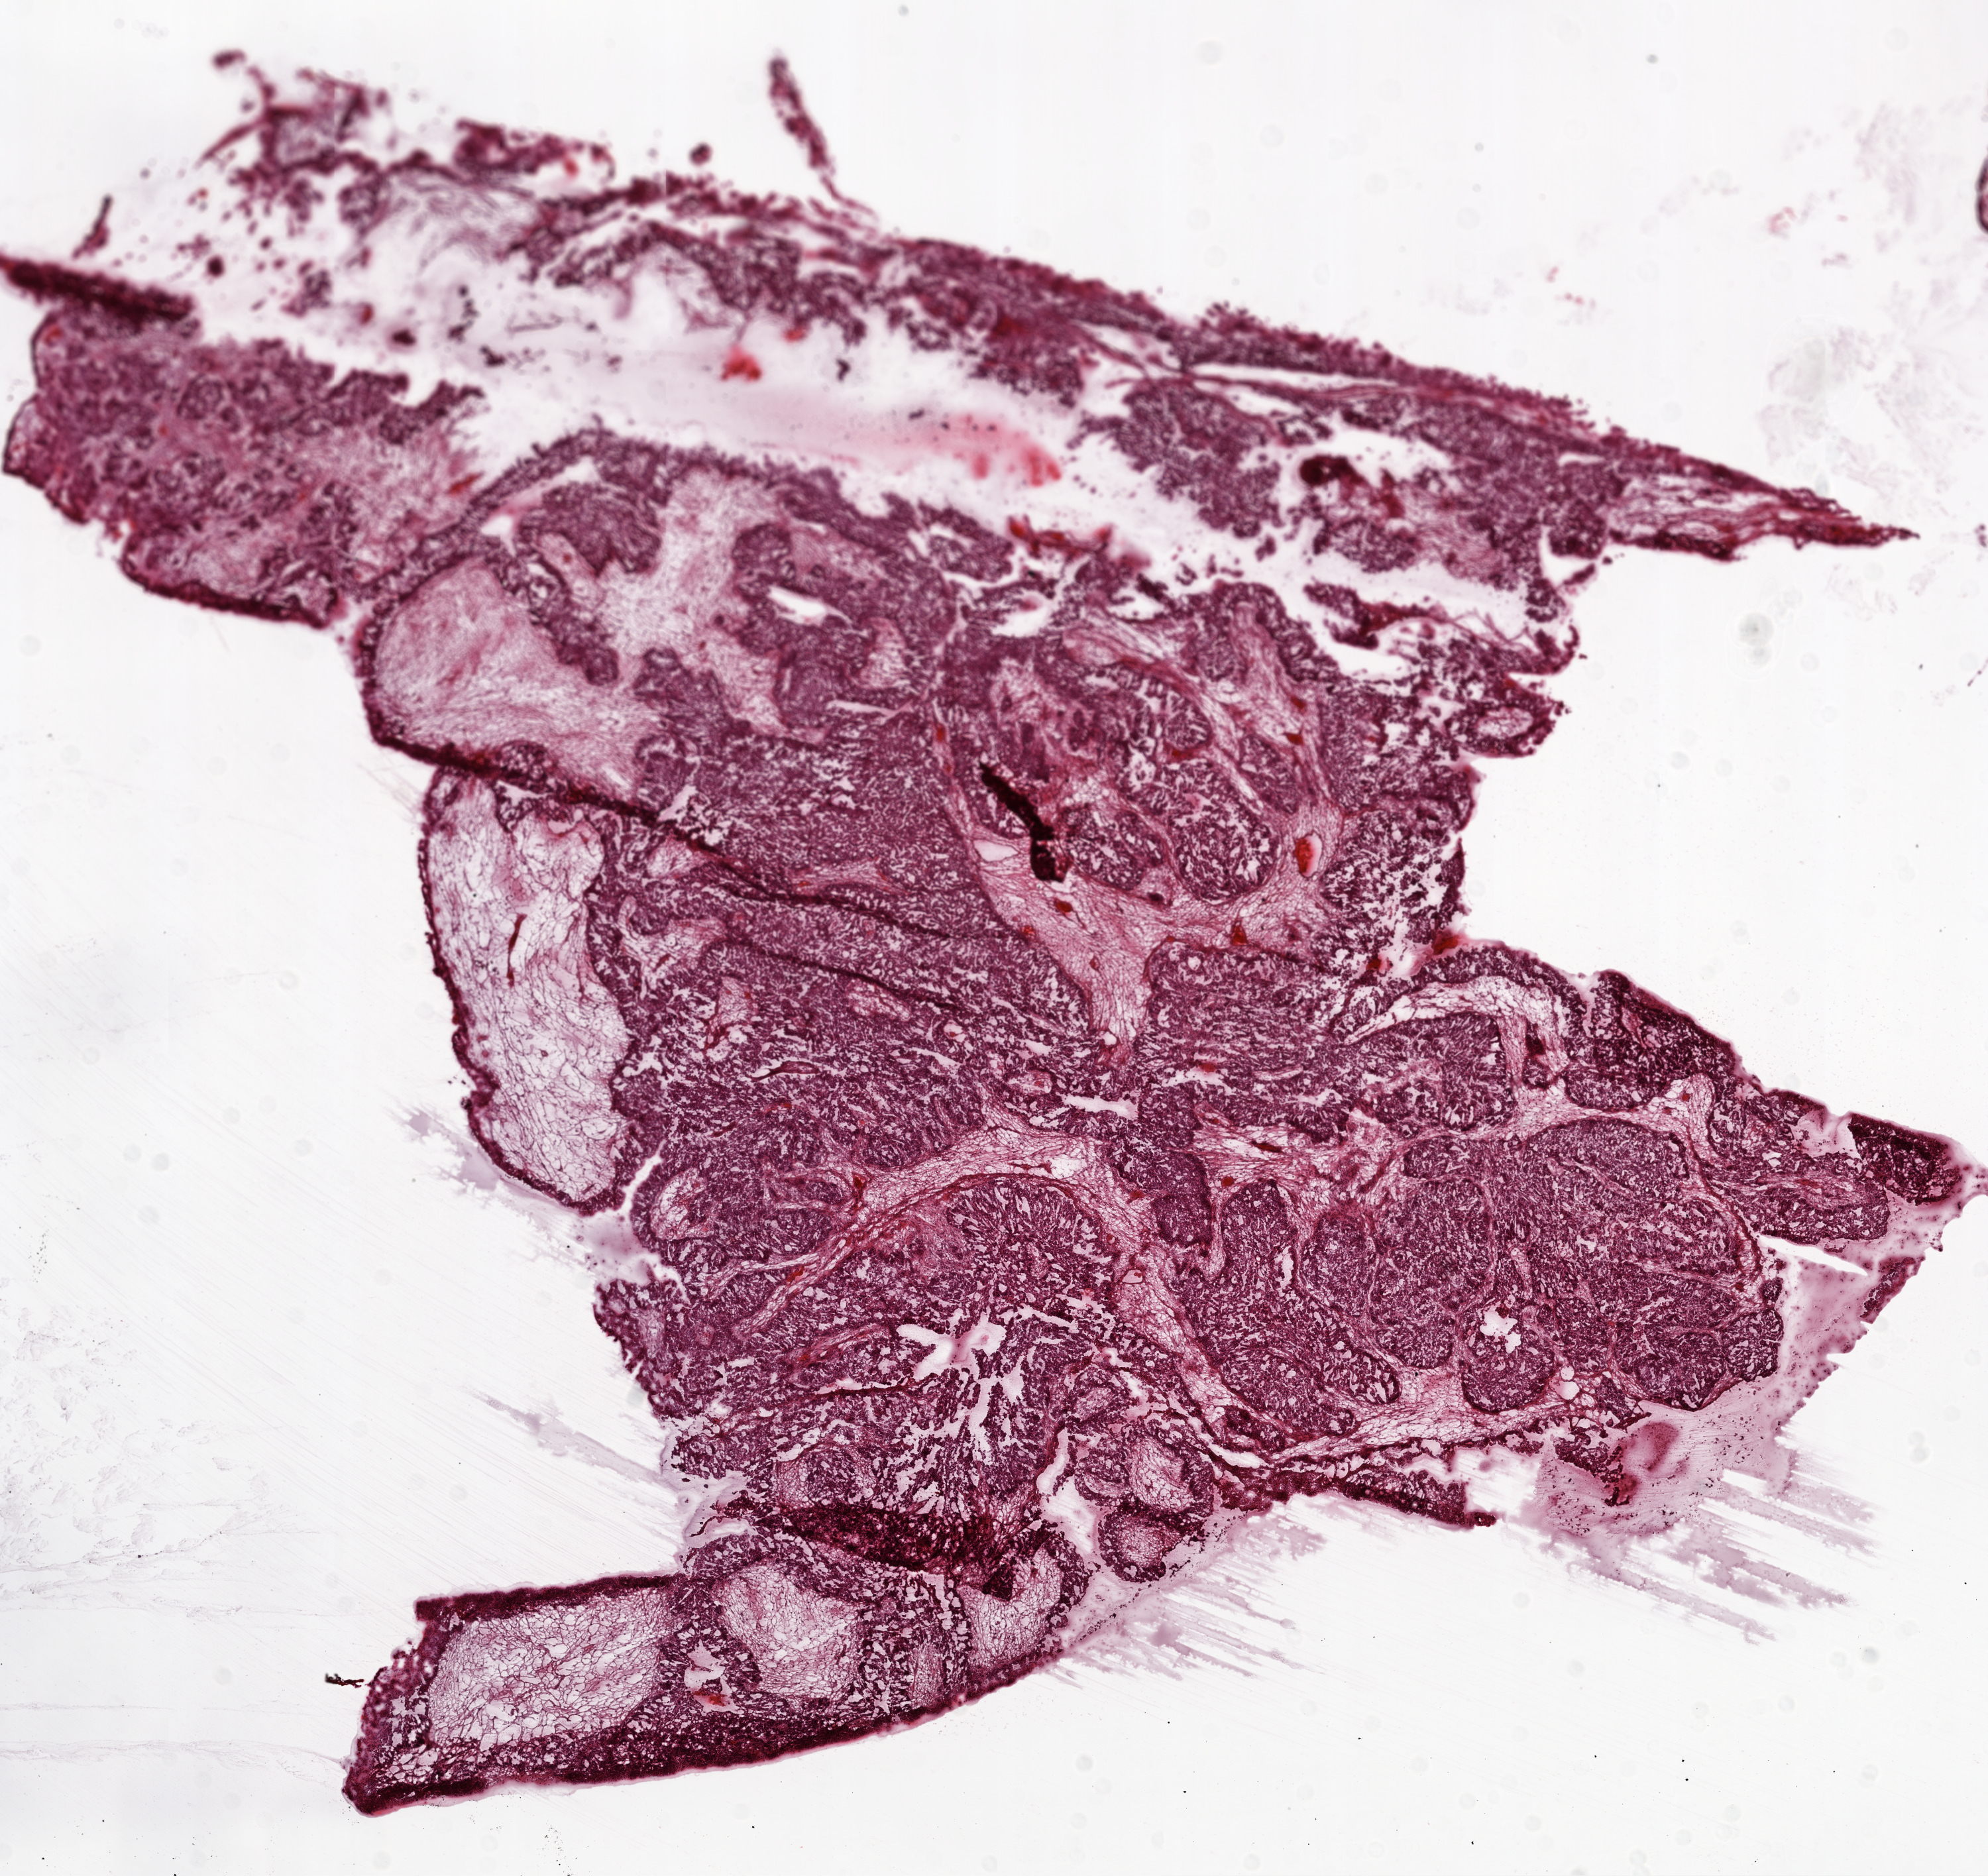
Whole-slide histology image, H&E-stained, a low-resolution overview of the entire scanned area, about 12.0 x 11.4 mm (acquisition: 20x scan). Frozen section from the top of the tissue portion. Primary tumour sample from the ovary. Female patient; age at initial diagnosis 54 years. Slide review estimates, as recorded: tumour cells 80%, tumour nuclei 90%.
Diagnosis: Serous cystadenocarcinoma, NOS.